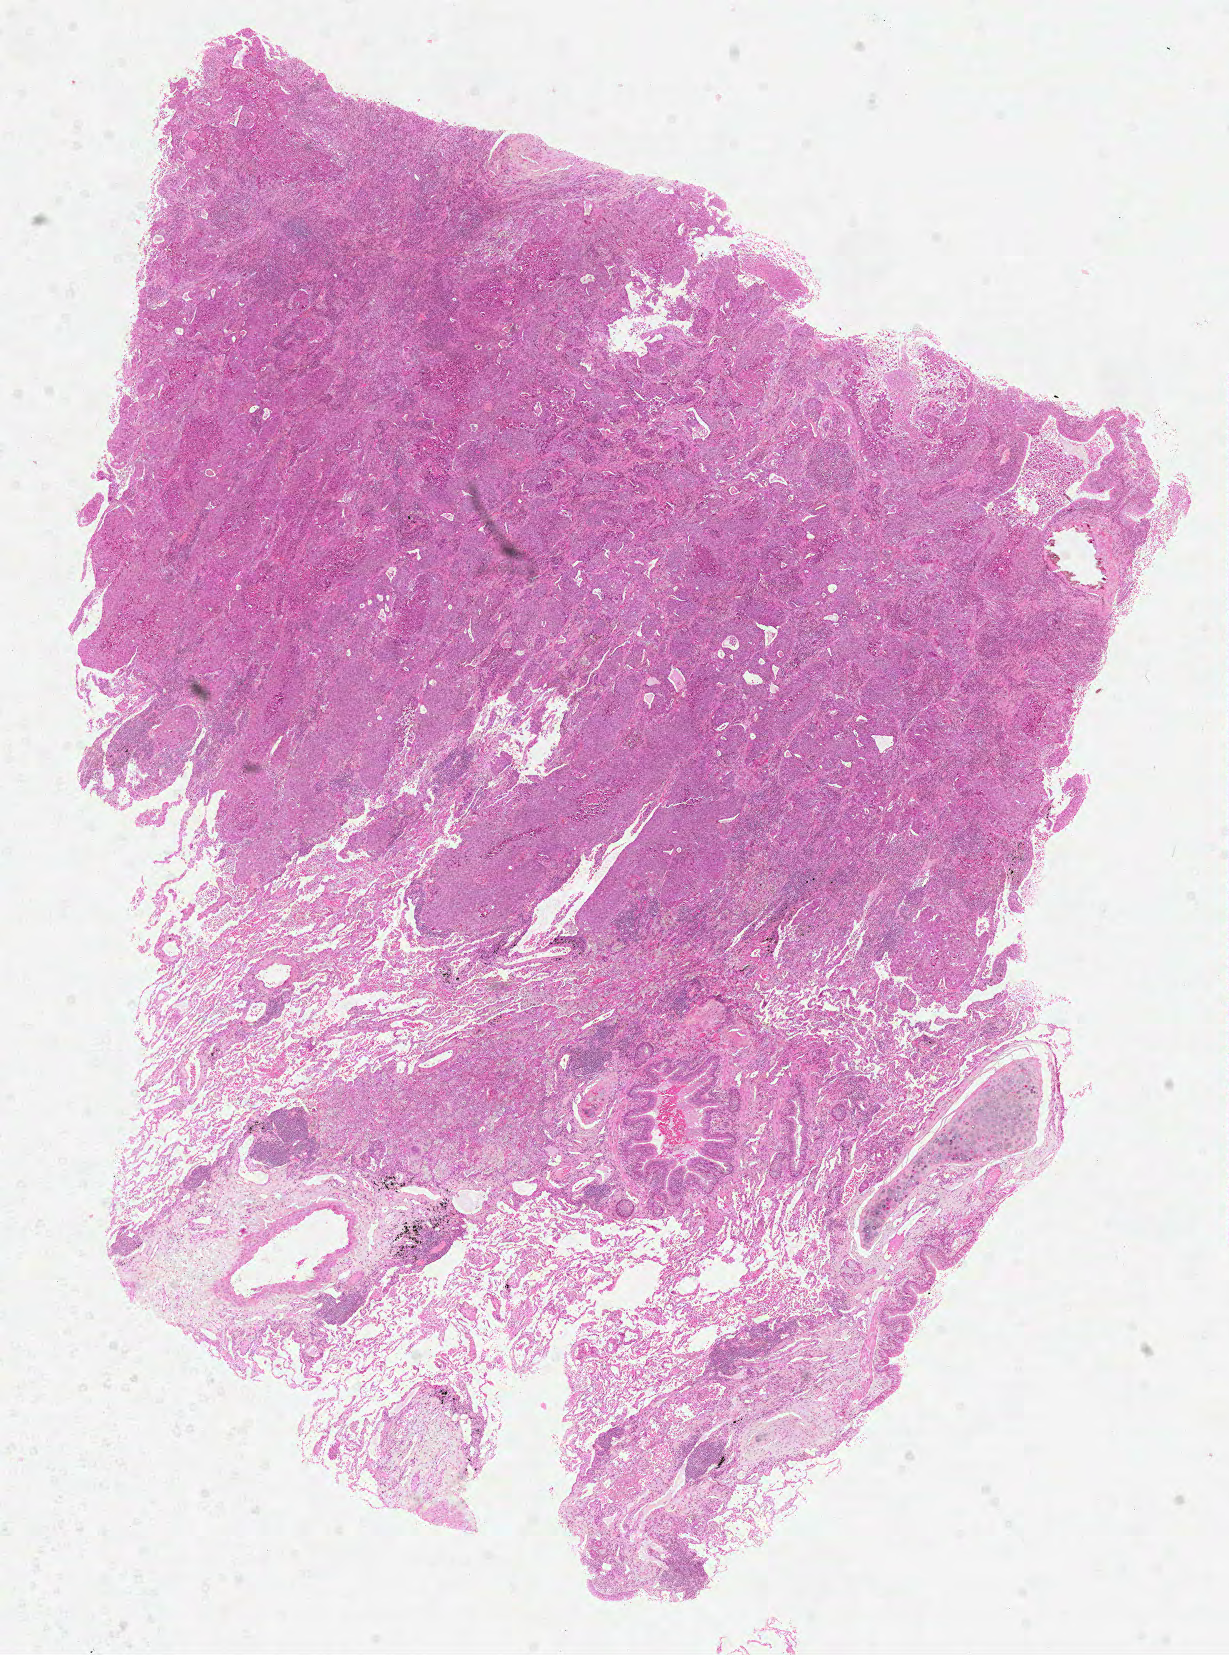
Hematoxylin and eosin (H&E) stained whole-slide image, shown as a low-resolution overview of the whole scanned area (about 9.9 x 13.3 mm), formalin-fixed paraffin-embedded (FFPE) diagnostic section, sample: primary tumour, lung. Patient: female, age at initial diagnosis 55 years.
Diagnosis: Squamous cell carcinoma, NOS. TNM: T2 N0 M0. AJCC pathologic stage: IB (5th edition).